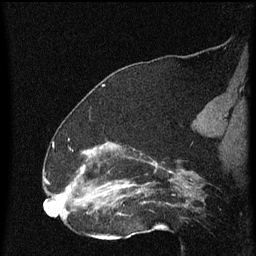
Breast MRI (dynamic contrast-enhanced), one sagittal slice; slice 35 of 60 in the series (ordered by position); dynamic contrast-enhanced series, image 2 of 4 at this slice position (ordered by acquisition); 1.5 T; TE 4.2 ms, TR 8 ms; 2 mm slice thickness; 256 × 256 image matrix. Patient: female, 52 years.
Outlined on this slice (semi-automatic segmentation, software-assisted and operator-edited):
- analysis volume of interest (the breast-tissue region the enhancement analysis was run in; not a lesion): box from (x=73, y=148) to (x=172, y=219) px
- tumour enhancement mask (voxels above the 70 % enhancement threshold inside the analysis volume of interest): (x=81, y=152)–(x=158, y=199)